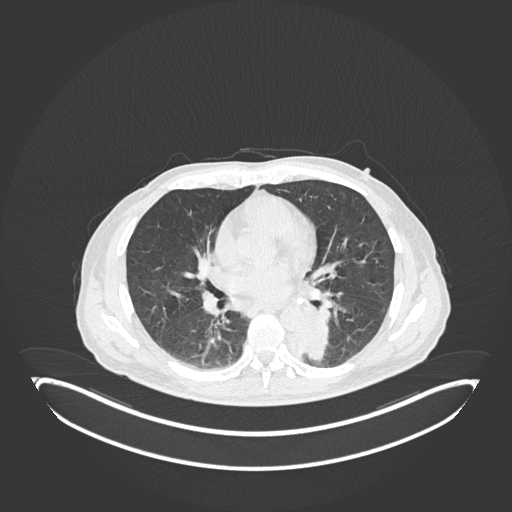
Chest CT, one axial slice. Position 96 of 251 along the scan axis. 120 kVp. Lung window (W 1500 / L -600 HU). 1 mm slice thickness. 512 × 512 image matrix, field of view 500 × 500 mm. Male patient, age 72 years. Case-level facts recorded for this patient, not image findings: clinical TNM (as recorded): T2b N0 M1.
Outlined on this slice (bounding box drawn by a radiologist):
- lung tumour (recorded histology: adenocarcinoma): bounding box <281,315,328,365> (left, top, right, bottom; pixels)